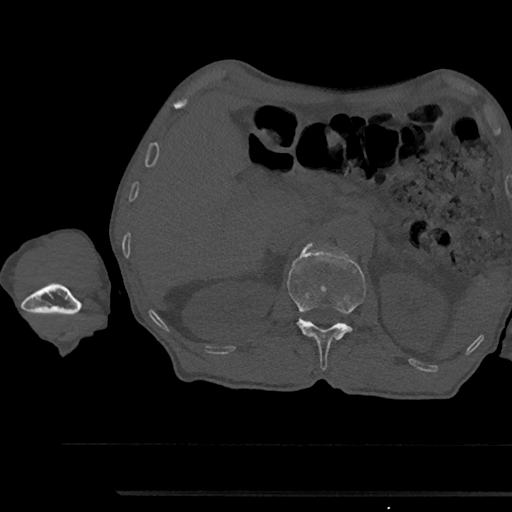
CT including the spine, one axial slice. Position 633 of 797 along the scan axis. Reconstruction kernel Br40s/3. 120 kVp. Bone window (W 1800 / L 400 HU). 0.5 mm slice thickness. 512 × 512 image matrix, field of view 367 × 367 mm. Male patient, age 79 years. Case-level facts recorded for this patient, not image findings: primary cancer: prostate.
Outlined on this slice (semi-automatic segmentation, software-assisted and operator-edited):
- L1 vertebra: bounding box [x1, y1, x2, y2] px = [287, 244, 366, 370]